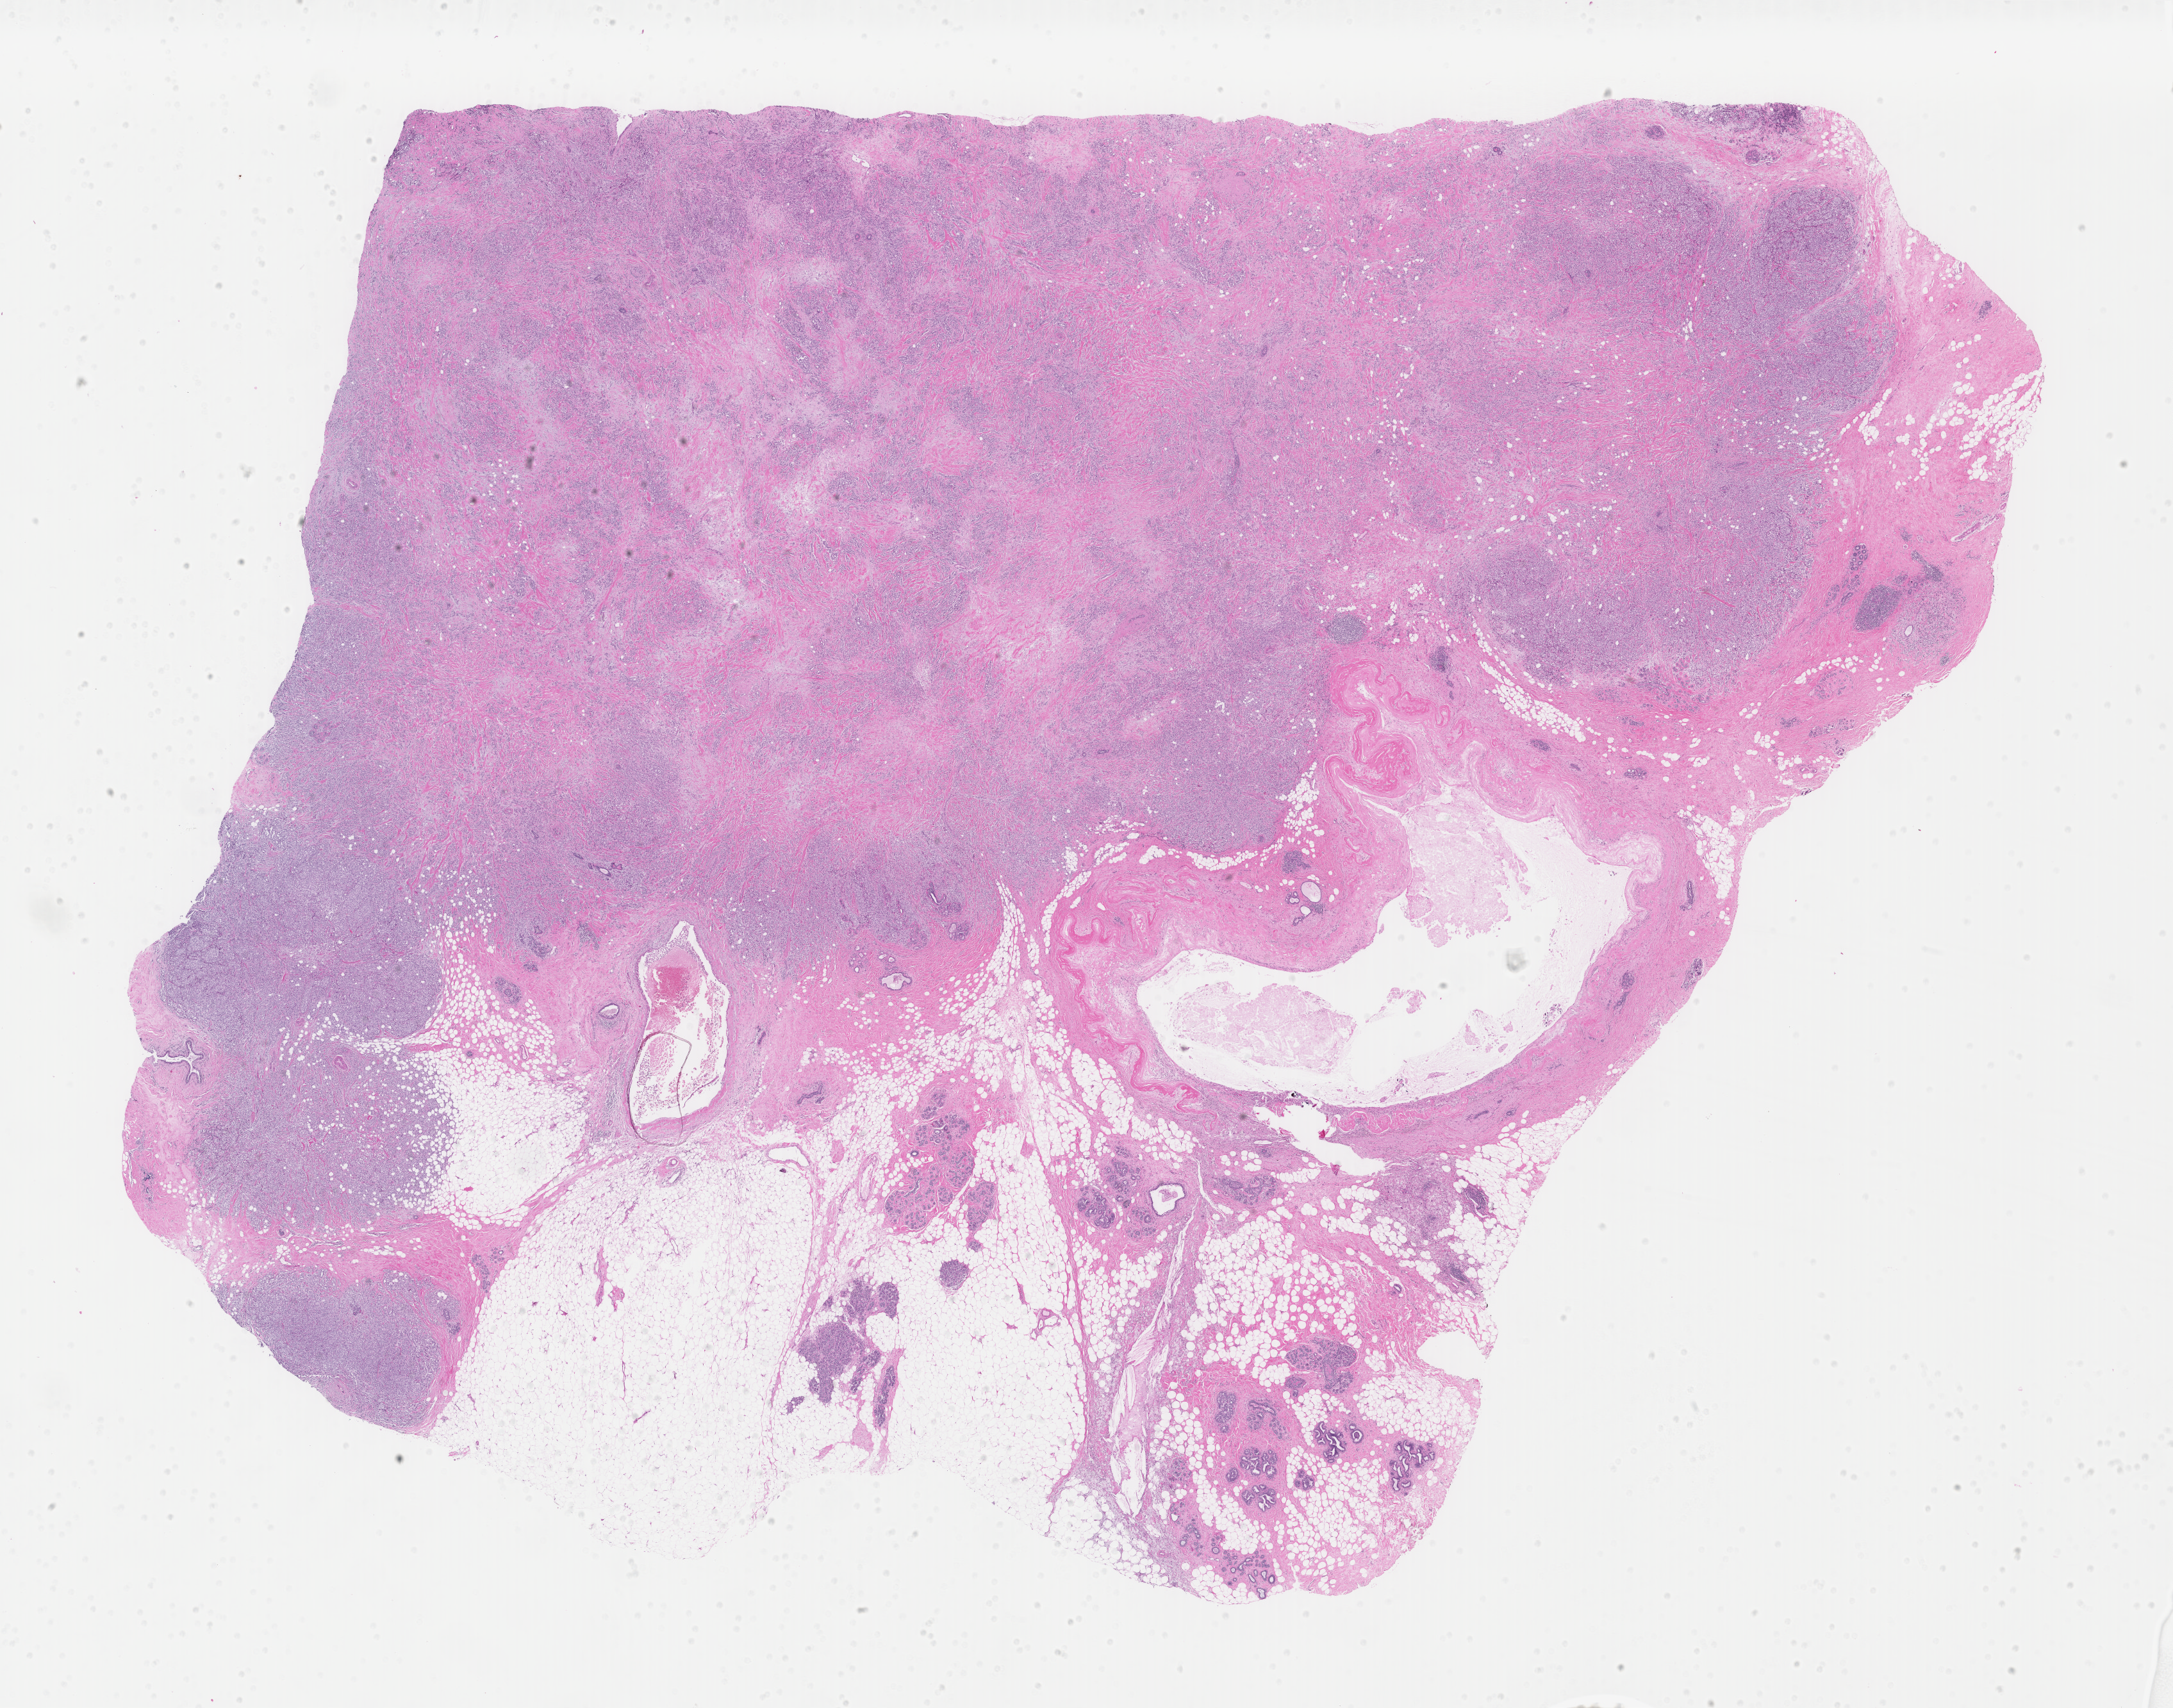
Whole-slide histology image, H&E, whole scanned area (about 26.9 x 21.2 mm) shown as a low-resolution overview; formalin-fixed paraffin-embedded (FFPE) diagnostic section; breast, primary tumour sample. Patient: female, age at initial diagnosis 50 years.
TNM: T3 N0 (i-) M0. Laterality: left. Lymph nodes positive (case pathology): 0 of 3 examined. AJCC pathologic stage: IIB. Pathologic diagnosis: Lobular carcinoma, NOS.